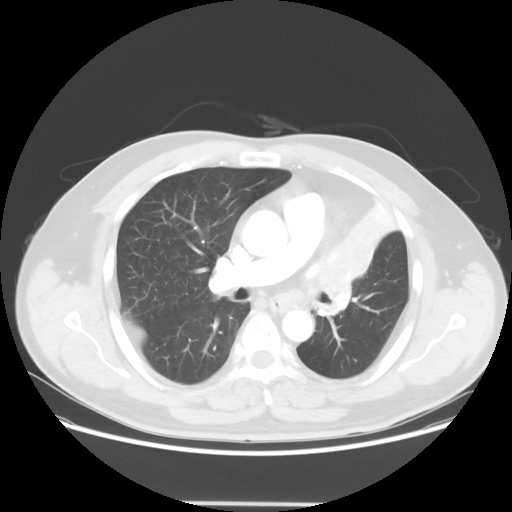
Chest CT, one axial slice; reconstruction kernel STANDARD; lung window (W 1500 / L -600 HU); 5 mm slice thickness; 512 × 512 image matrix, field of view 403 × 403 mm. Male patient, age 49 years. Case-level facts recorded for this patient, not image findings: clinical TNM (as recorded): T3 N3 M1c.
Annotated regions visible in this slice (rectangle marked by the reading radiologist):
- lung tumour (recorded histology: squamous cell carcinoma): bounding box [x1, y1, x2, y2] px = [313, 233, 378, 334]